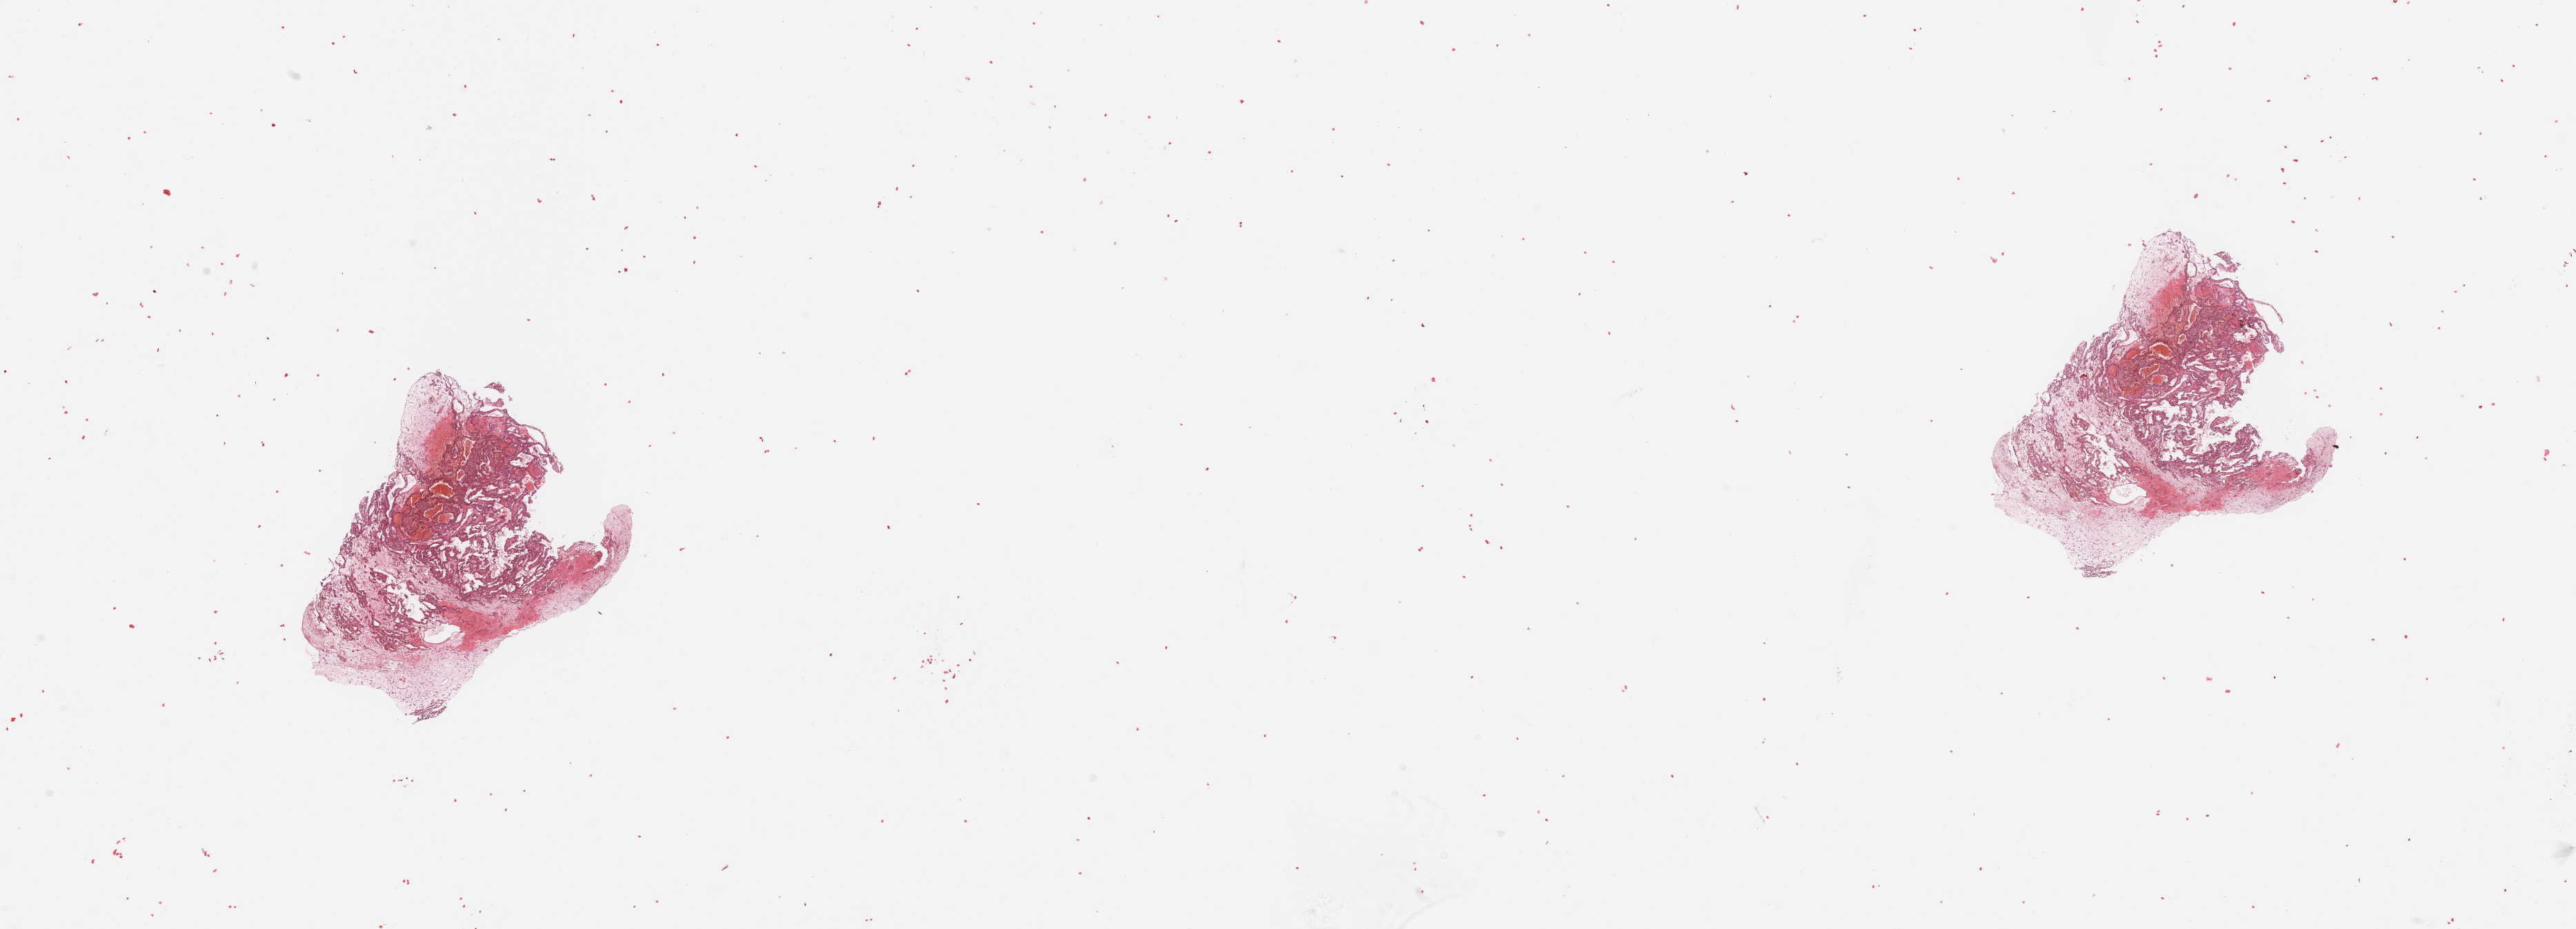
Whole-slide histology image, H&E, a low-resolution overview of the entire scanned area, about 29.5 x 10.6 mm (slide scanned at 20x); tumour tissue sample, sampled site: kidney. 67-year-old male patient. Histologic grade: G2 (moderately differentiated). Composition of this section per pathologist review: tumour nuclei 85%, necrosis 5%.
* AJCC pathologic stage: I
* primary tumour site (as recorded): middle
* histologic diagnosis: Renal cell carcinoma, NOS